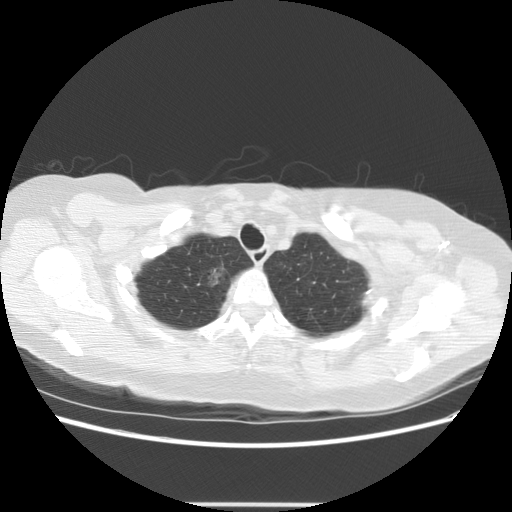
Low-dose screening chest CT, one axial slice; slice 111 of 126 in the series (ordered by position); reconstruction kernel STANDARD; lung window (W 1500 / L -600 HU); 2.5 mm slice thickness; 512 × 512 image matrix, field of view 360 × 360 mm.
Outlined on this slice (outlined manually by an expert reader):
- lesion 1 (tumor, upper lobe of right lung): bounding box (x1, y1, x2, y2) in pixels: (207, 268, 222, 286)